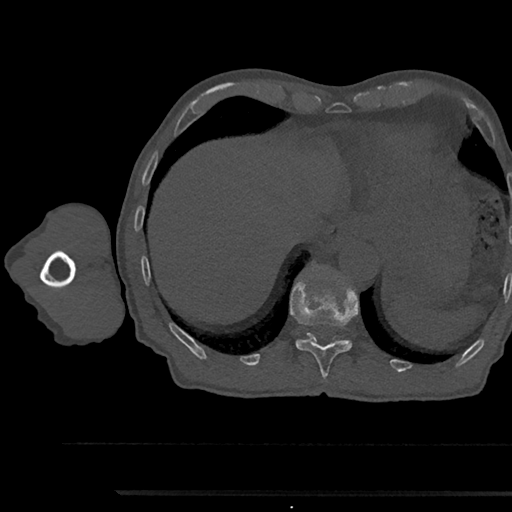
CT including the spine, one axial slice. Slice 771 of 797 in the series (ordered by position). Bone window (W 1800 / L 400 HU). 0.5 mm slice thickness. 512 × 512 image matrix, field of view 367 × 367 mm. Patient: male, 79 years. Case-level facts recorded for this patient, not image findings: primary cancer: prostate.
Annotated regions visible in this slice (semi-automatic segmentation, software-assisted and operator-edited):
- T11 vertebra: box from (x=291, y=284) to (x=358, y=381) px
- T12 vertebra: (x=308, y=334)–(x=311, y=336)